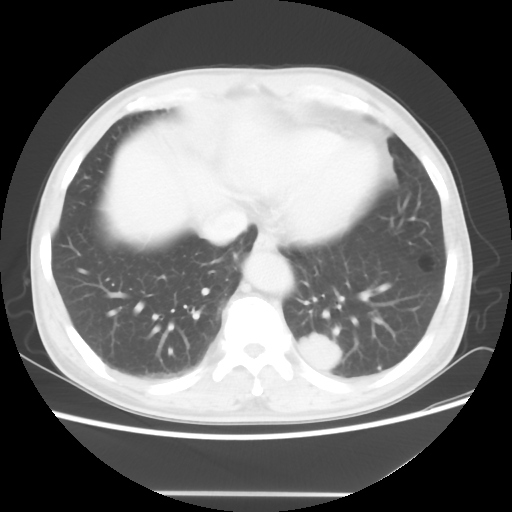
Chest CT, one axial slice. Slice 15 of 60 in the series (ordered by position). Lung window (W 1500 / L -600 HU). 5 mm slice thickness. 512 × 512 image matrix, field of view 360 × 360 mm. Male patient, age 55 years. Case-level facts recorded for this patient, not image findings: clinical TNM (as recorded): T1c N3 M0.
Annotated regions visible in this slice (rectangle marked by the reading radiologist):
- lung tumour (recorded histology: small cell carcinoma): bounding box <295,330,342,374> (left, top, right, bottom; pixels)